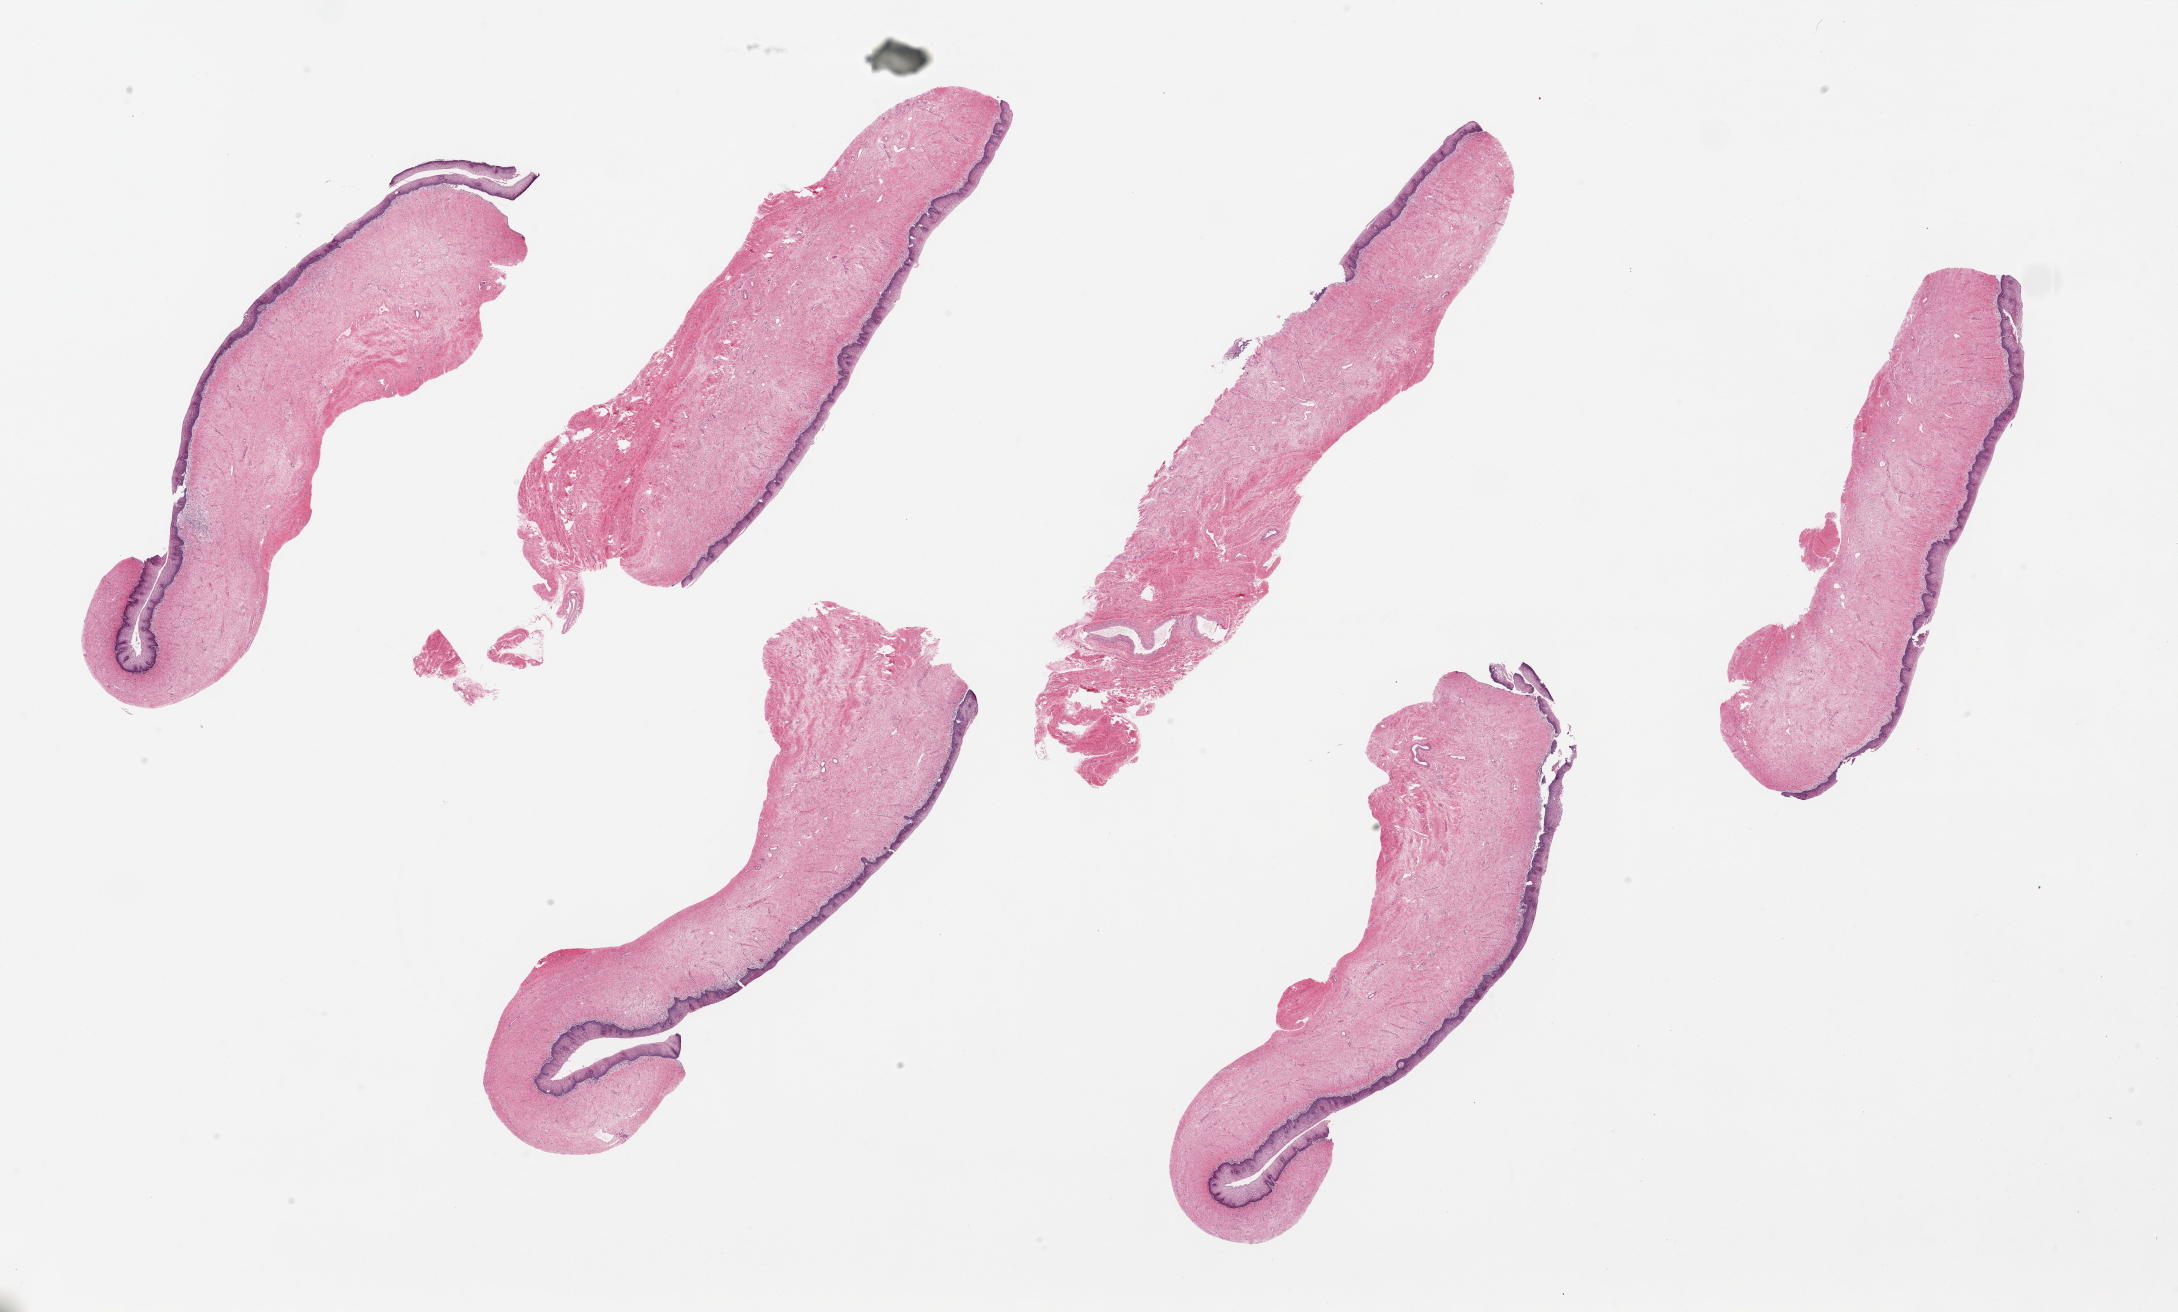
Haematoxylin and eosin whole-slide image — shown as a low-resolution overview of the whole scanned area (about 34.5 x 20.8 mm), PAXgene-fixed paraffin-embedded (PFPE) section, sampled site (target tissue): vagina, donor tissue sample. Female donor.
Pathologist's review note for this sample: 6 pieces, up to 13x3mm; squamous epithelium ~10% thickness.